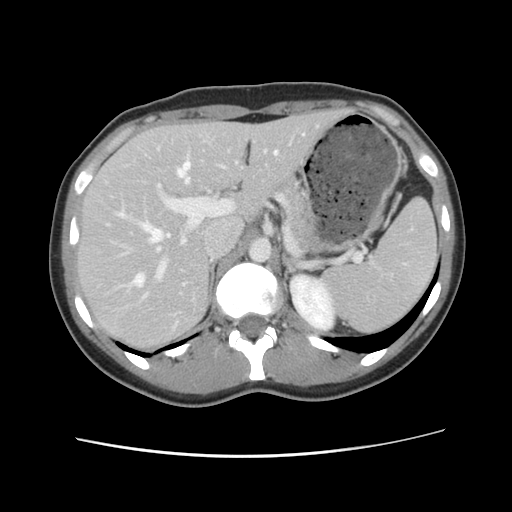
Contrast-enhanced abdominal CT, one axial slice. Position 71 of 134 along the scan axis. Intravenous contrast given. Soft-tissue window (W 400 / L 40 HU). 2.5 mm slice thickness. 512 × 512 image matrix, field of view 339 × 339 mm. Female patient, age 33 years. Case-level facts recorded for this patient, not image findings: diagnosis: colorectal cancer liver metastases, imaged before liver resection; multiple liver metastases: yes; largest metastasis: 4.5 cm; disease in both lobes: yes.
Outlined on this slice (outlined manually by an expert reader):
- hepatic veins: bounding box (x1, y1, x2, y2) in pixels: (119, 151, 278, 297)
- liver: (78, 110, 344, 352)
- planned liver remnant (the part of the liver to remain after resection): (78, 111, 343, 351)
- portal vein (with intrahepatic branches): (155, 138, 293, 274)